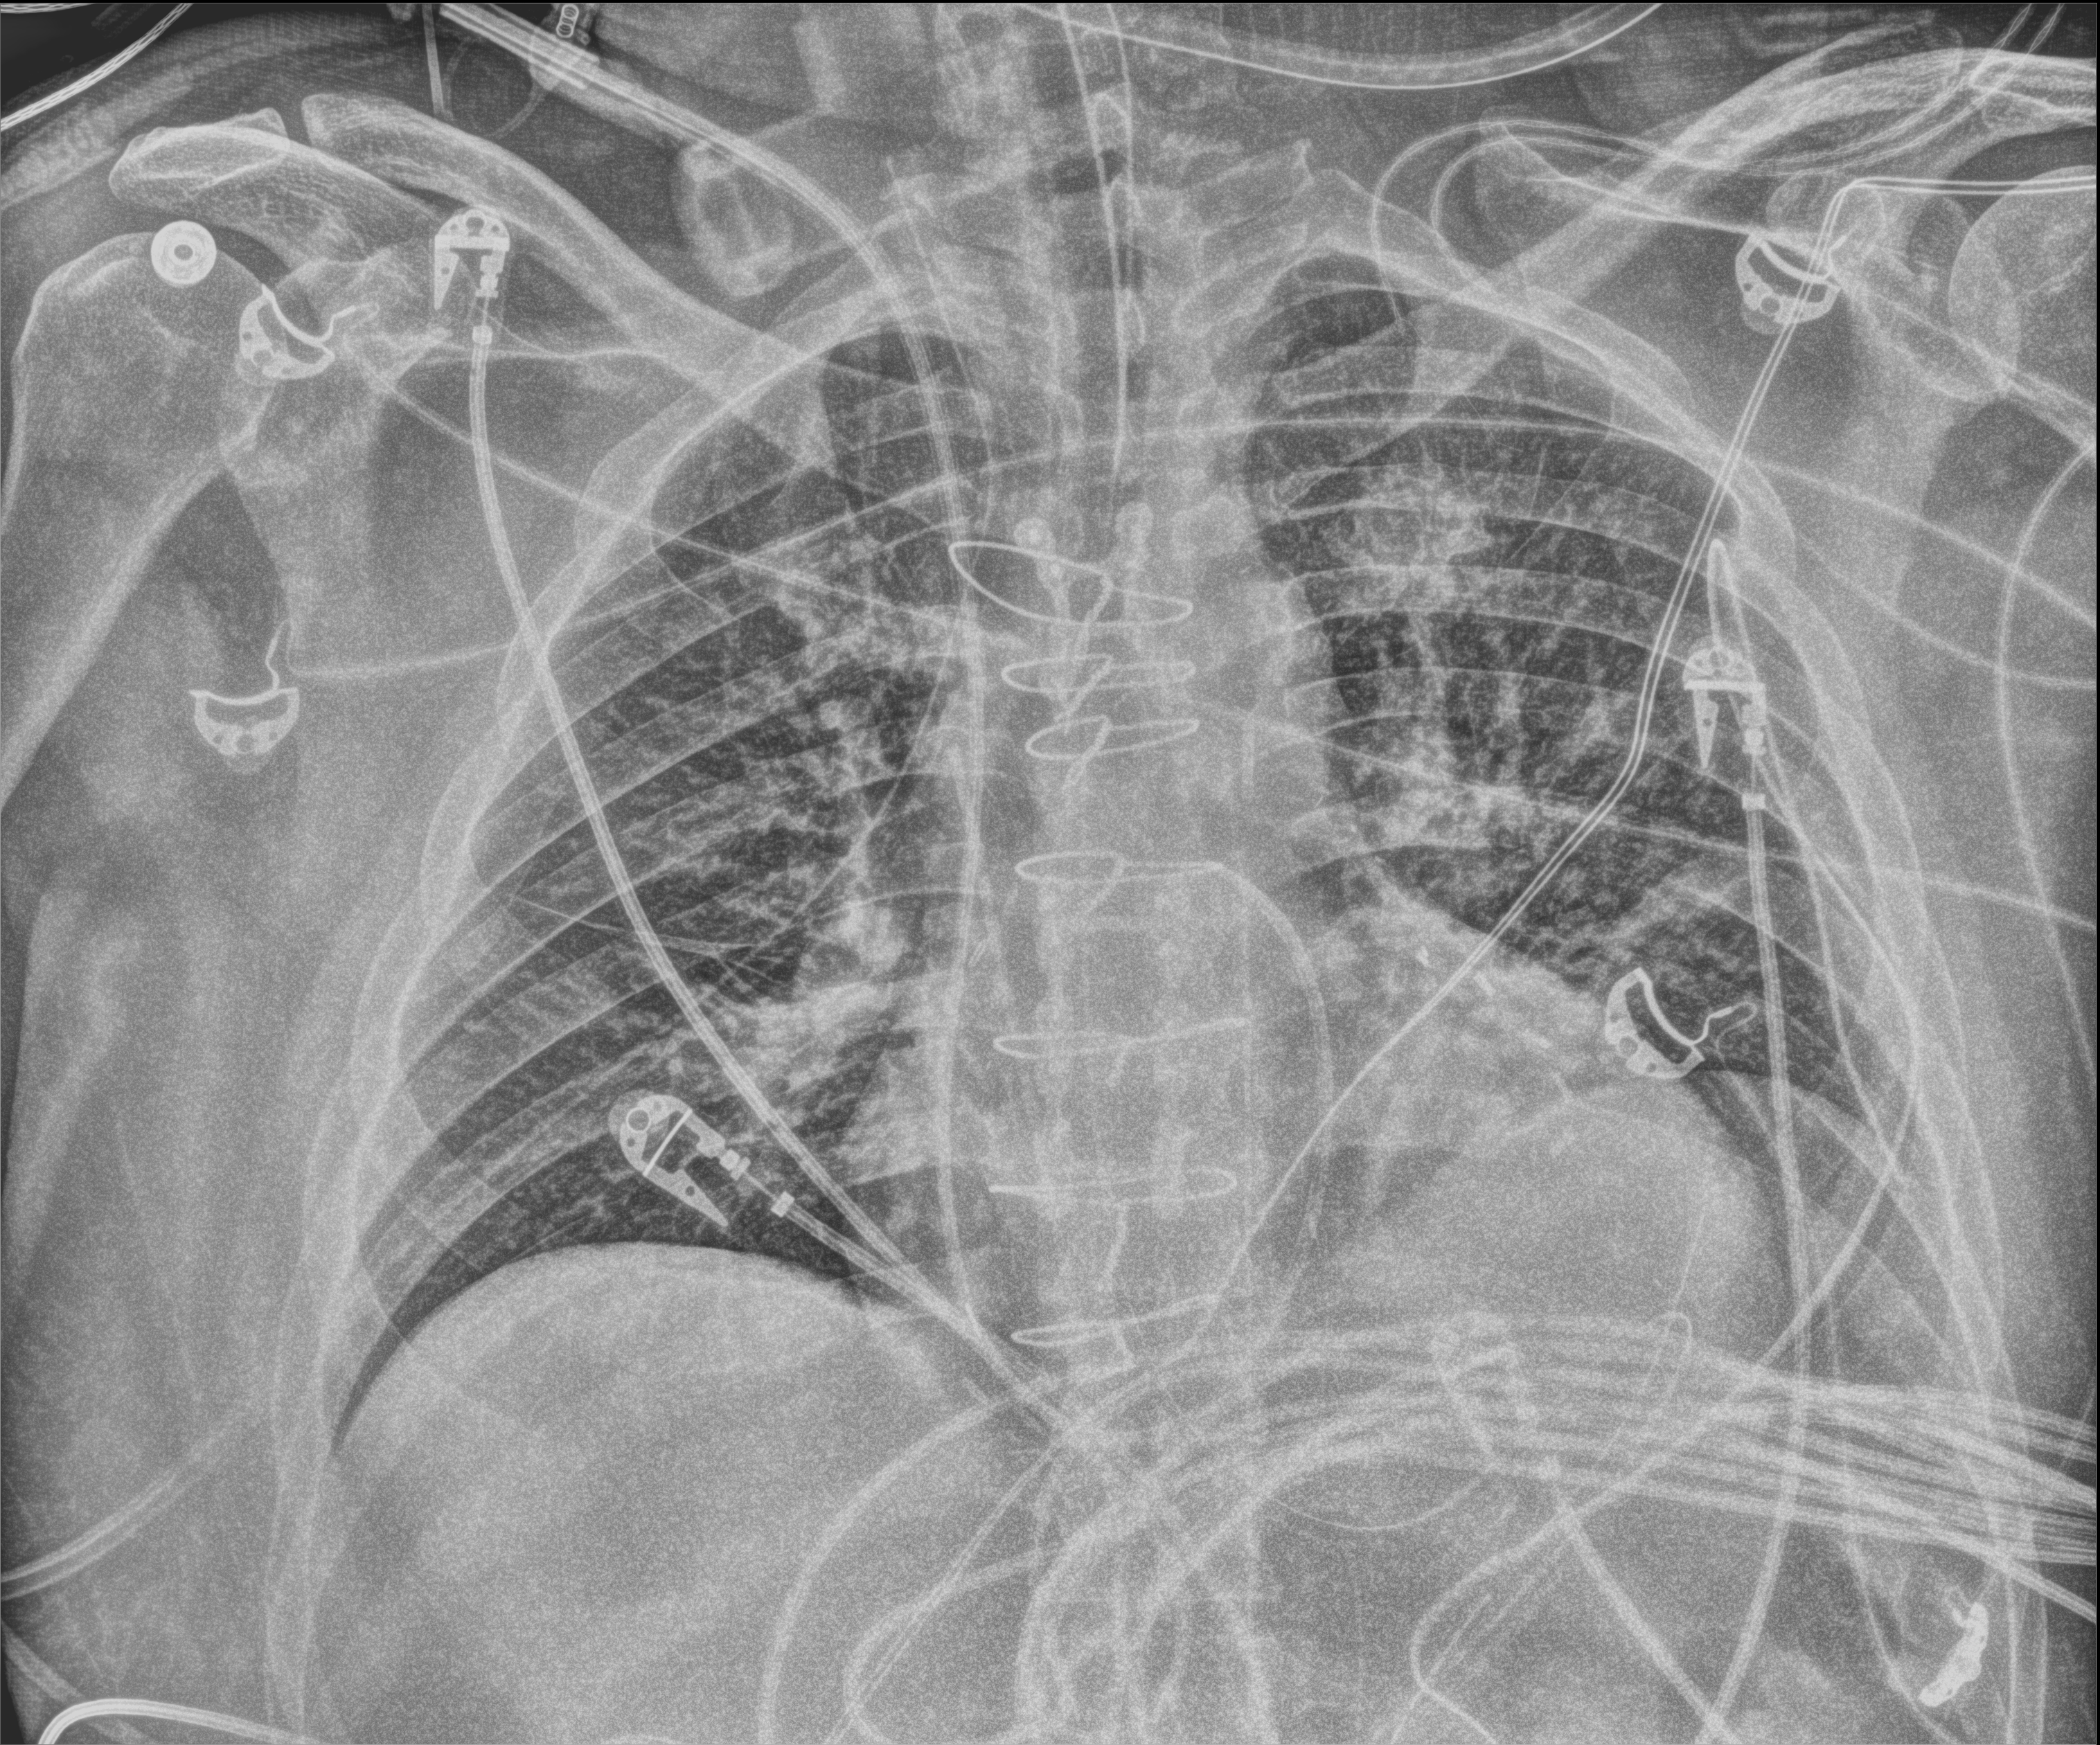
Bedside chest radiograph (digital radiography); anteroposterior (AP) projection. Patient hospitalised with COVID-19; male, aged 18–59 years.
Admission-level facts for this patient (not findings on this image; timing relative to this image not recorded): mechanically ventilated during this hospital stay: no.